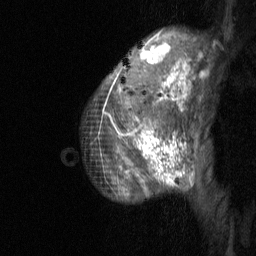
Breast MRI (dynamic contrast-enhanced), one sagittal slice; dynamic contrast-enhanced study with each time point stored as its own series, time point 2 of 3 at this slice position (early post-contrast, ordered by acquisition time); 1.5 T; TE 4.8 ms, TR 27 ms; 256 × 256 image matrix, field of view 180 × 180 mm. Patient: female, 36 years. From the clinical record (not read from this slice): setting: breast cancer imaged before/during neoadjuvant chemotherapy; receptor status: HR-positive, HER2-negative.
Outlined on this slice (semi-automatically segmented with operator editing):
- analysis volume of interest (the breast-tissue region the enhancement analysis was run in; not a lesion): bounding box <83,28,207,203> (left, top, right, bottom; pixels)
- tumour enhancement mask (voxels above the 90 % enhancement threshold inside the analysis volume of interest): <118,43,194,185>